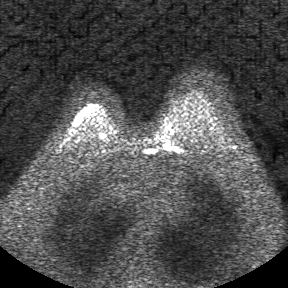
Breast MRI, one axial slice; slice 29 of 34 in the series (ordered by position); diffusion-weighted series; image 2 of 4 stored at this slice position (different b-values; order by instance number); 1.5 T; 288 × 288 image matrix, field of view 340 × 340 mm. Female patient.
Structures marked on this image (manually delineated by an expert):
- tumour on diffusion-weighted imaging: box from (x=82, y=108) to (x=90, y=112) px